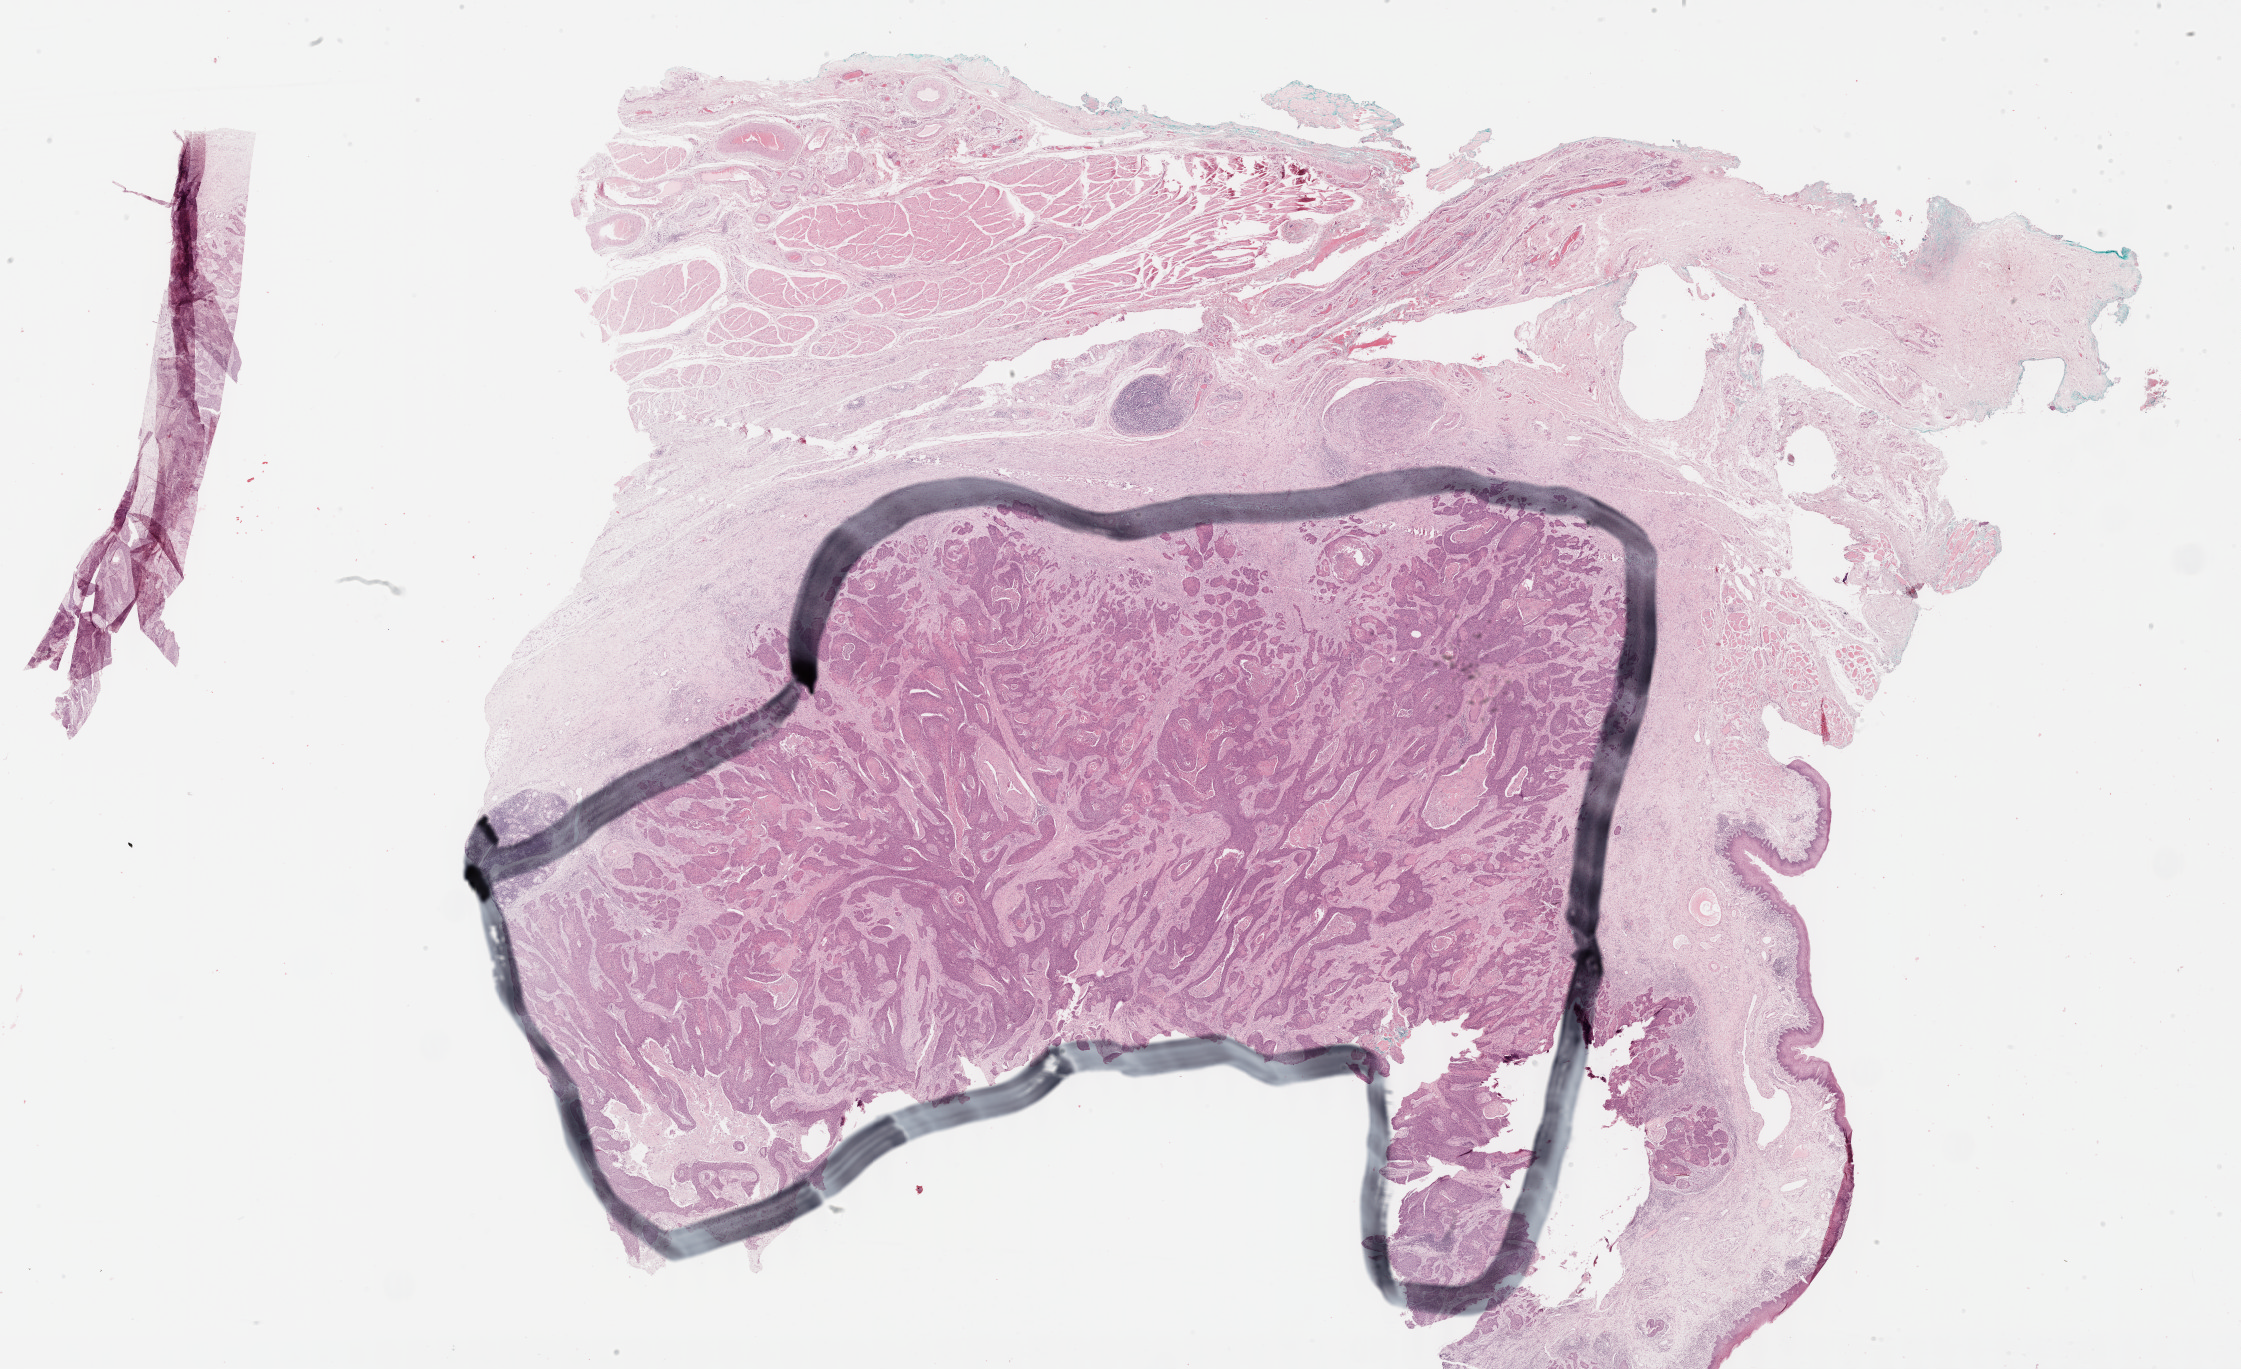
Hematoxylin and eosin (H&E) stained whole-slide image, low-resolution overview of the scanned area, about 36.2 x 22.1 mm (from a 40x scan), formalin-fixed paraffin-embedded (FFPE) diagnostic section, primary tumour sample from the head and neck. Patient: male, age at initial diagnosis 64 years. Histologic grade: G2 (moderately differentiated).
Diagnosis: Squamous cell carcinoma, NOS. Lymph nodes positive (case pathology): 2 of 47 examined.